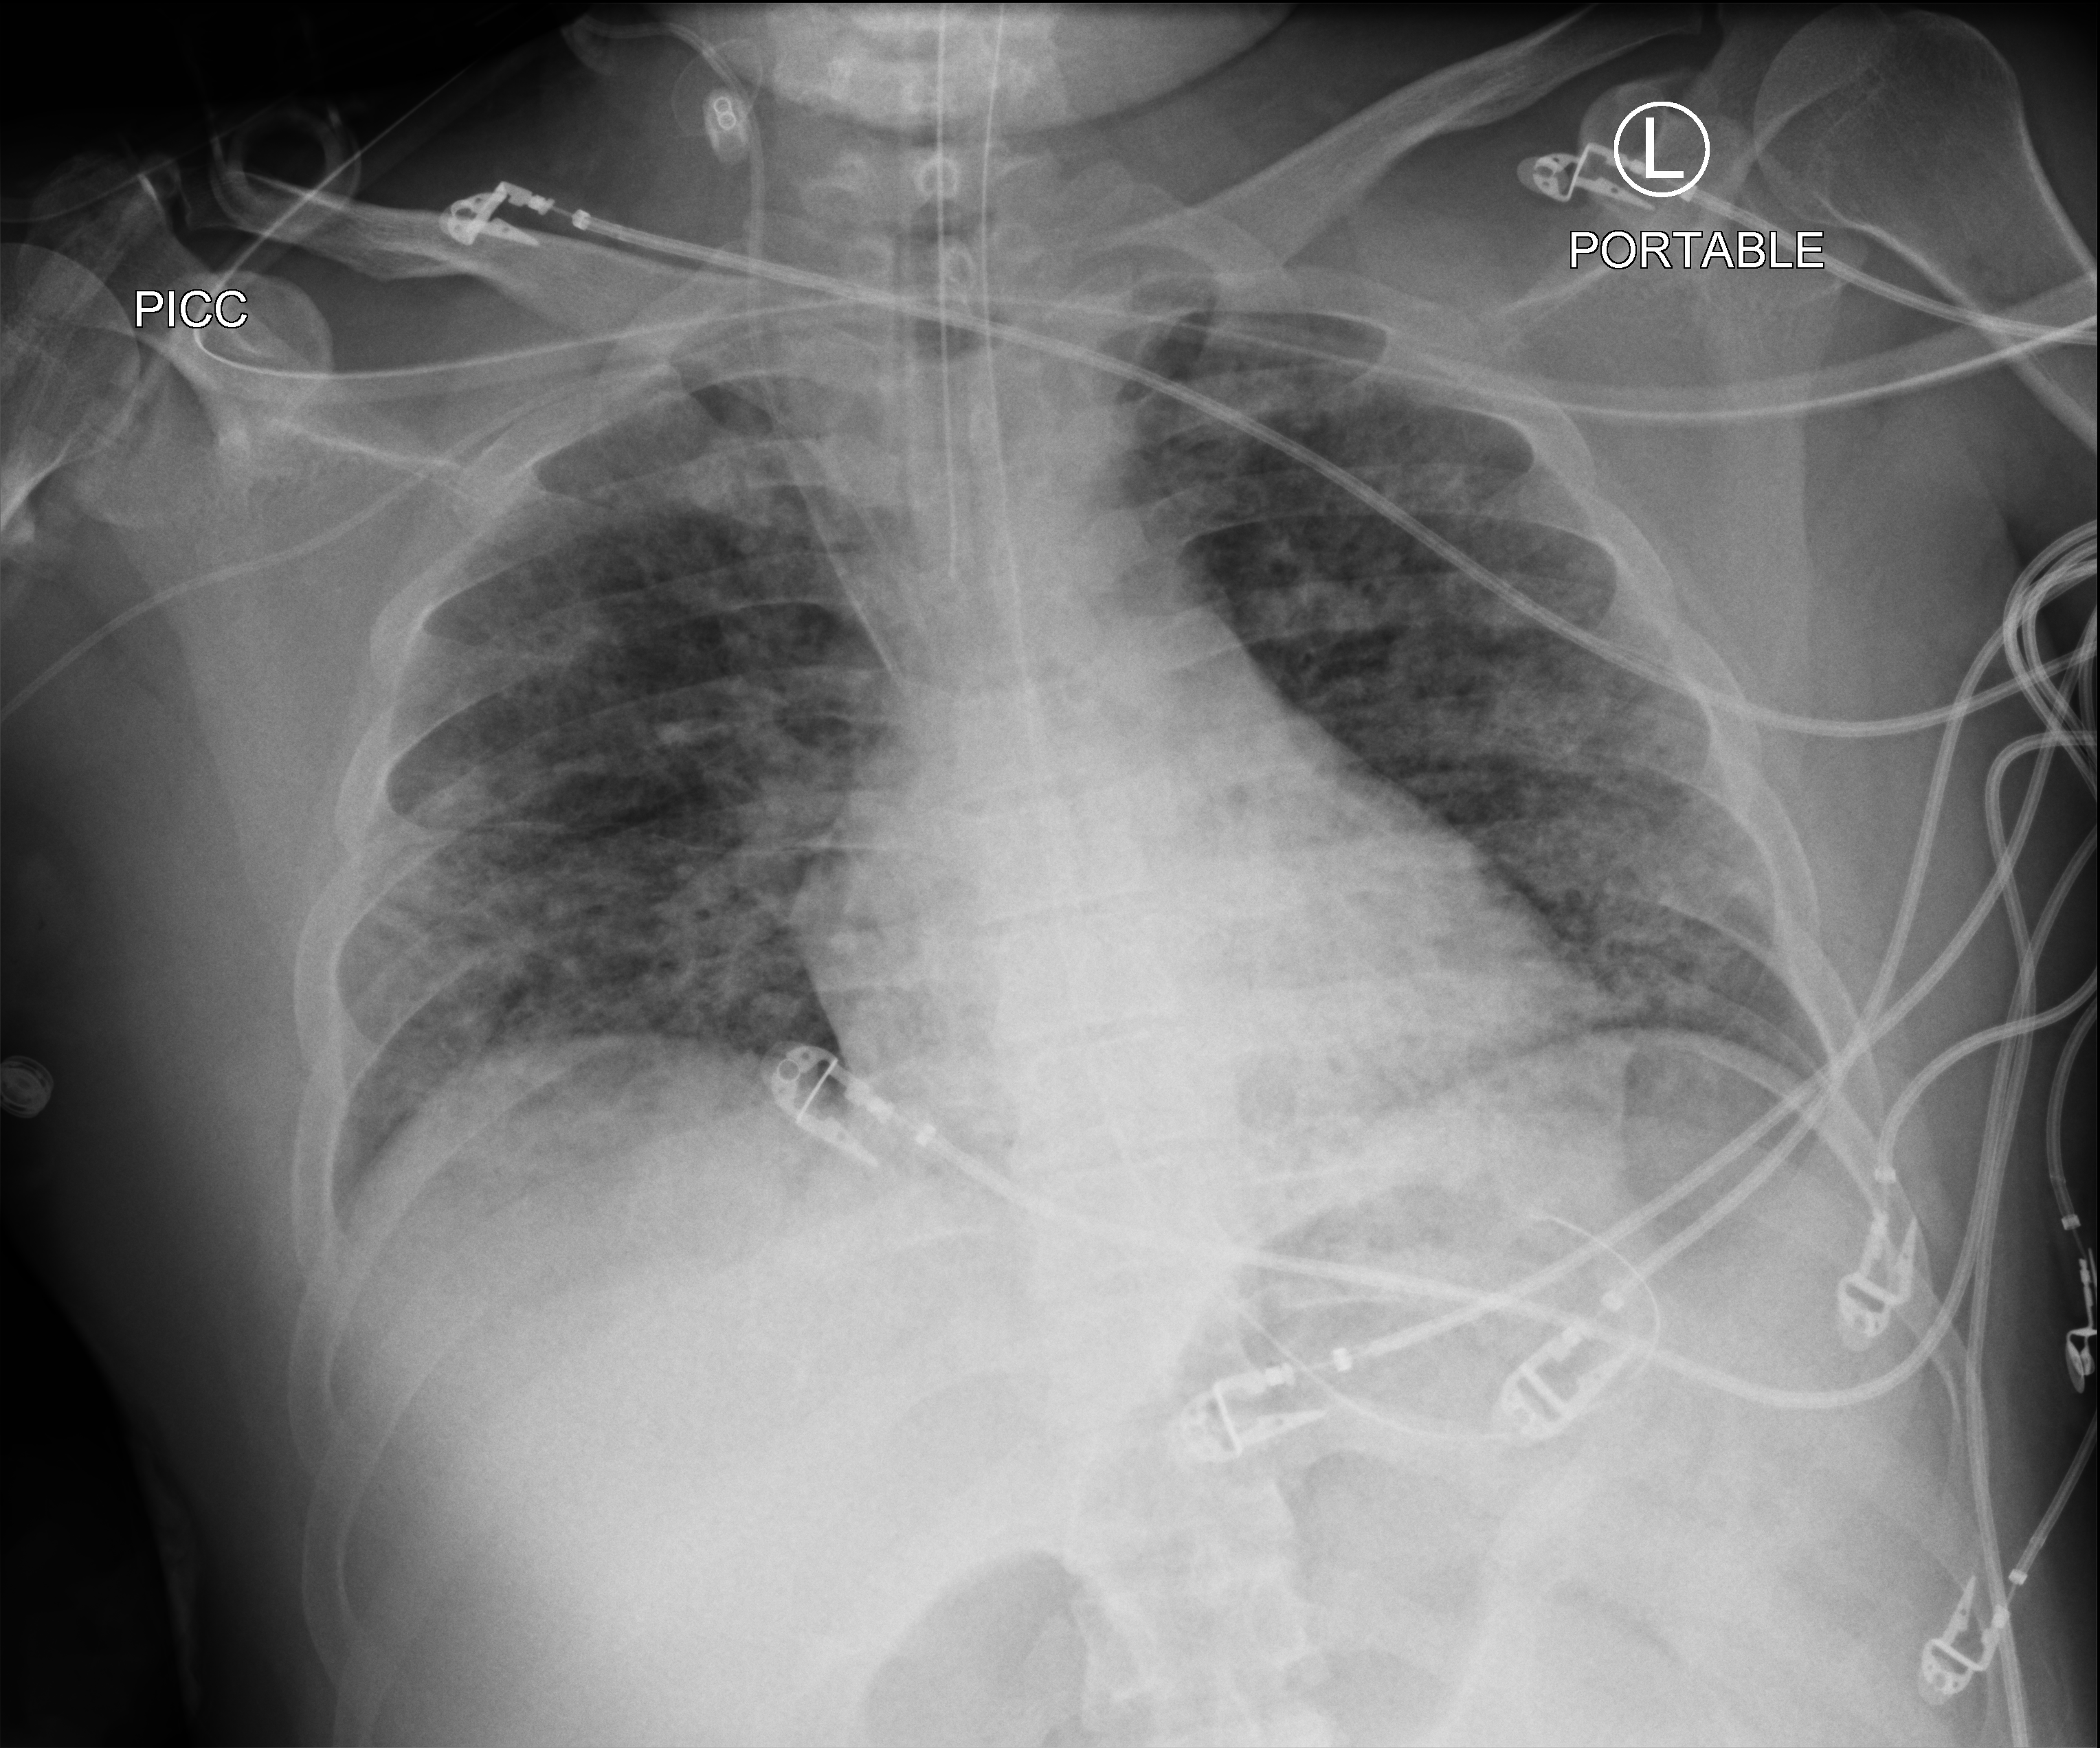
Bedside chest radiograph (computed radiography), anteroposterior (AP) projection. Male patient hospitalised with COVID-19, age 18–59 years.
Admission-level facts for this patient (not findings on this image; timing relative to this image not recorded):
- chronic kidney disease (admission record): no
- admitted to intensive care during this hospital stay: yes
- length of hospital stay: 44 days